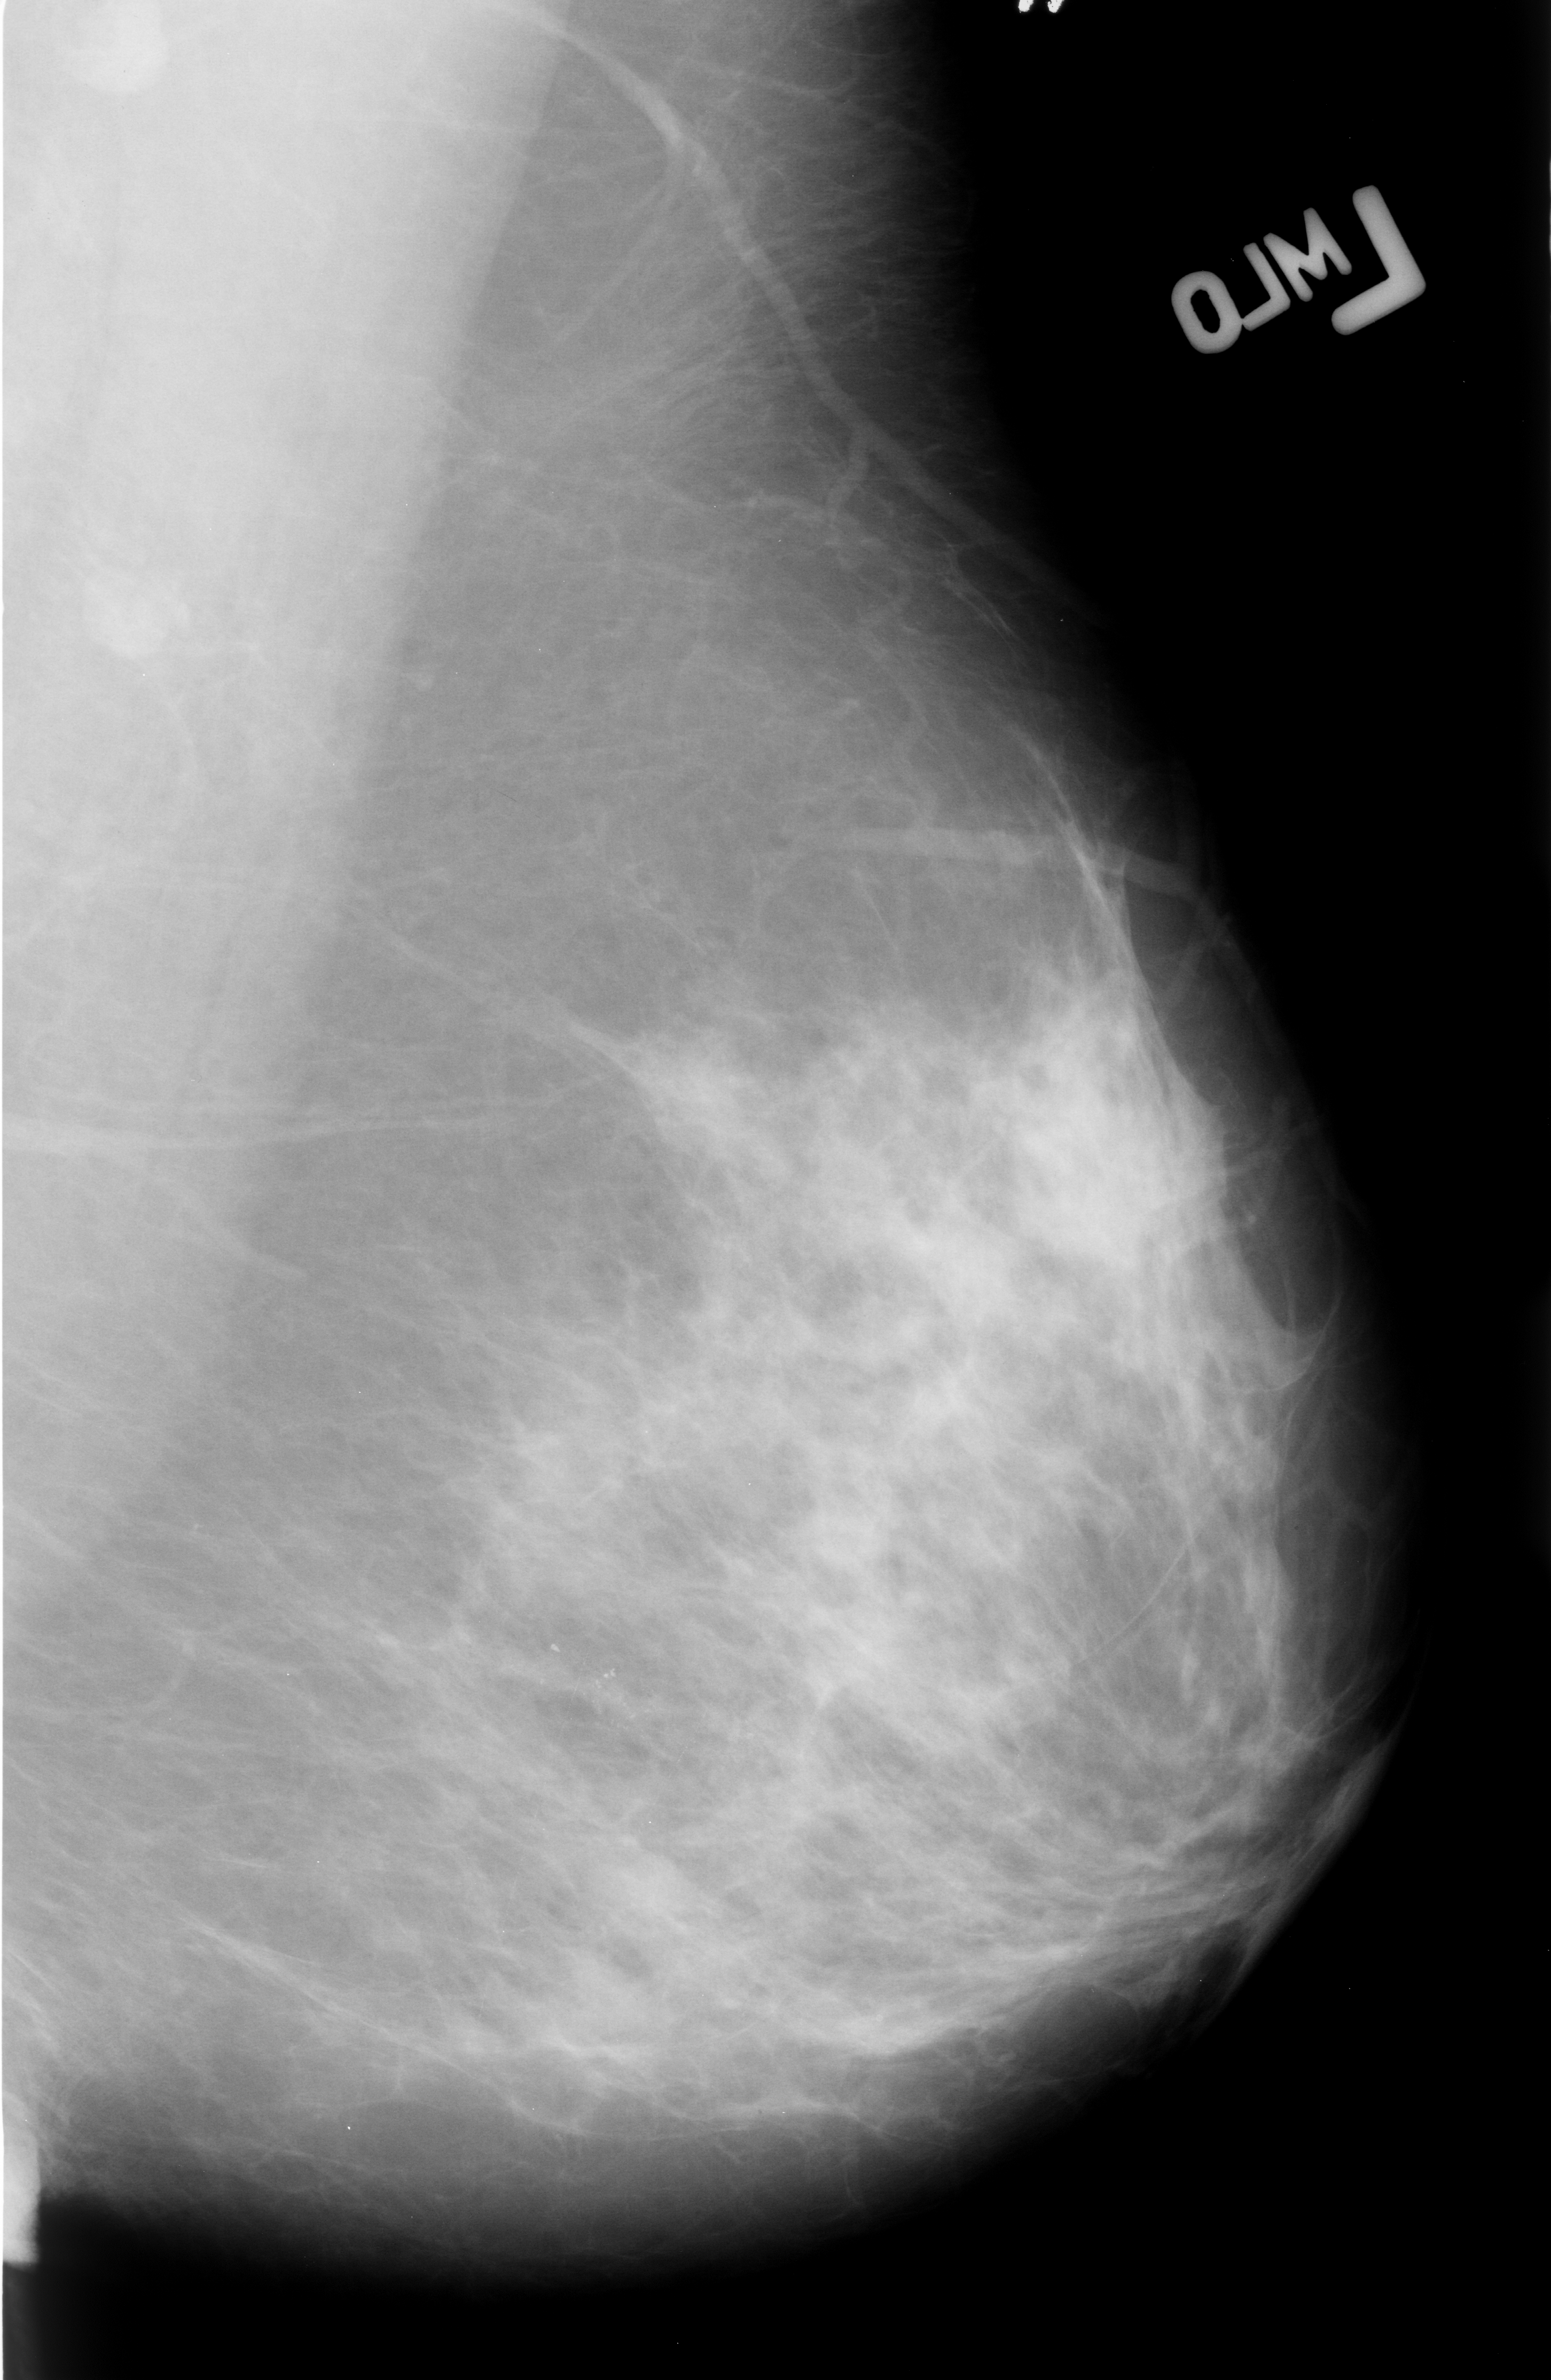
Scanned film-screen mammogram; left breast; MLO view; BI-RADS breast density category 2 (scale 1–4).
Abnormality record for this image: calcifications, morphology pleomorphic, distribution clustered; BI-RADS assessment category 4; pathology (as recorded): malignant.